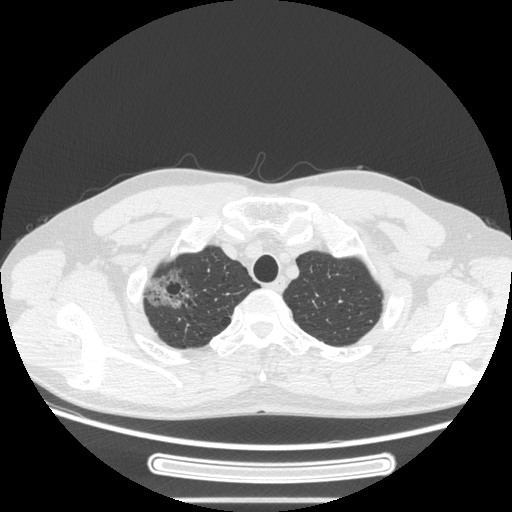
Chest CT, one axial slice. Position 230 of 269 along the scan axis. Reconstruction kernel STANDARD. 120 kVp. Lung window (W 1500 / L -600 HU). 512 × 512 image matrix. Patient: male, 53 years. Case-level facts recorded for this patient, not image findings: clinical TNM (as recorded): T1c N0 M0.
Structures marked on this image (bounding box drawn by a radiologist):
- lung tumour (recorded histology: adenocarcinoma): bounding box (x1, y1, x2, y2) in pixels: (134, 256, 201, 315)